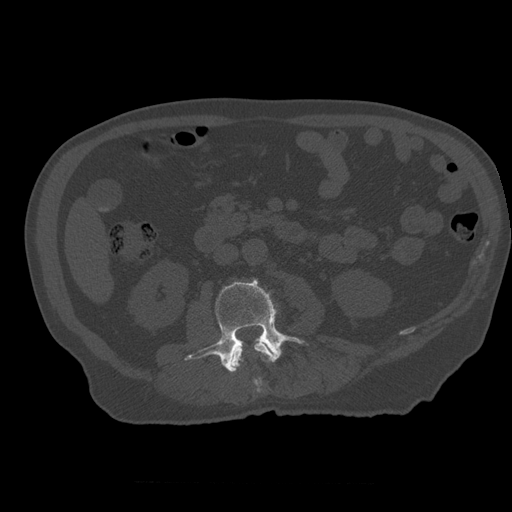
CT including the spine, one axial slice; slice 195 of 399 in the series (ordered by position); 120 kVp; bone window (W 1800 / L 400 HU); 1.25 mm slice thickness; 512 × 512 image matrix, field of view 407 × 407 mm. Patient age 73 years. From the clinical record (not read from this slice): primary cancer: prostate; vertebrae with lytic lesions (as recorded): L2.
Outlined on this slice (semi-automatically segmented with operator editing):
- L2 vertebra: bounding box <231,341,274,393> (left, top, right, bottom; pixels)
- L3 vertebra: <186,278,304,372>